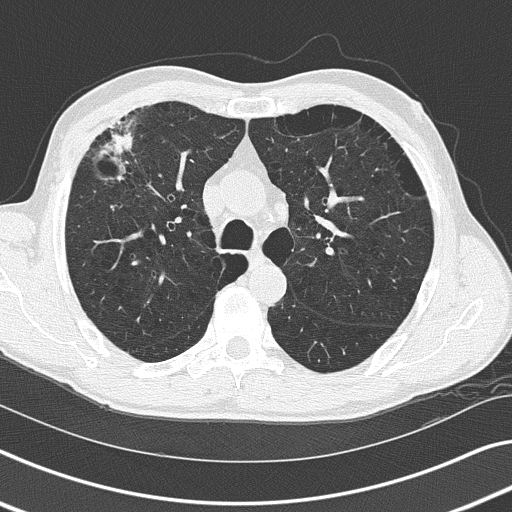
Axial slice from a low-dose chest CT screening exam; third annual screen; lung window (W 1500 / L -600 HU); lung (sharp) reconstruction kernel (B50f); 120 kVp; slice 61 of 170 in the series. Male participant, aged 66 years at enrolment. Current smoker at enrolment.
Expert-annotated lung lesion, box from (x=81, y=110) to (x=155, y=194) px. The exam's reader record, not a measurement of the box and not confirmed to be the same lesion: non-calcified nodule or mass ≥4 mm, left lower lobe, 9 × 8 mm, smooth margins, soft tissue attenuation, pre-existing on the prior screen: yes; interval growth: no. Note: the box lies in the patient's right hemithorax on this image, whereas the reader's record names the left lung; they may be different findings.